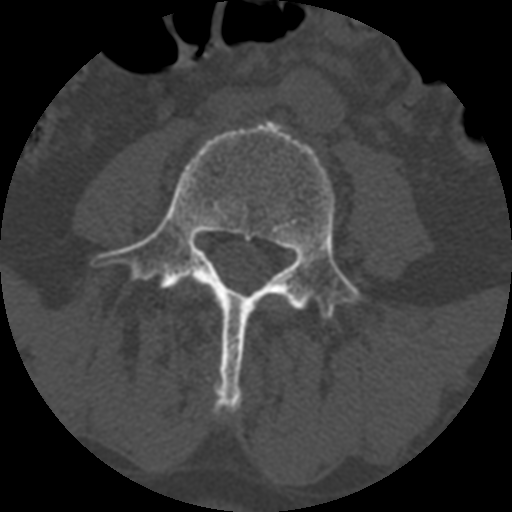
CT including the spine, one axial slice. Position 284 of 399 along the scan axis. Bone window (W 1800 / L 400 HU). 1.25 mm slice thickness. 512 × 512 image matrix, field of view 160 × 160 mm. Patient age 71 years. Case-level facts recorded for this patient, not image findings: primary cancer: prostate.
Annotated regions visible in this slice (semi-automatically segmented with operator editing):
- L4 vertebra: bounding box (x1, y1, x2, y2) in pixels: (92, 121, 370, 416)